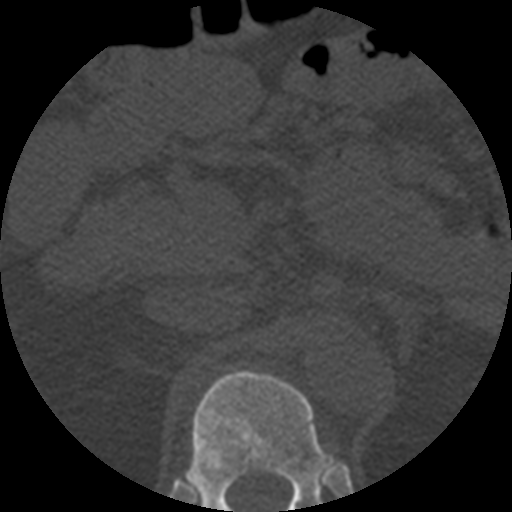
CT including the spine, one axial slice; position 216 of 508 along the scan axis; bone window (W 1800 / L 400 HU); 1.25 mm slice thickness; 512 × 512 image matrix, field of view 160 × 160 mm. Patient age 57 years. Case-level facts recorded for this patient, not image findings: primary cancer: prostate.
Structures marked on this image (semi-automatic segmentation, software-assisted and operator-edited):
- T12 vertebra: bounding box [x1, y1, x2, y2] px = [186, 370, 336, 512]